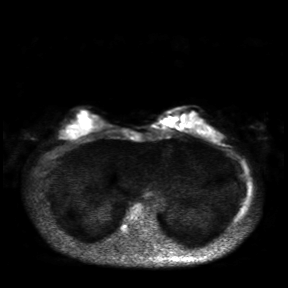
Breast MRI, one axial slice. Position 9 of 30 along the scan axis. Diffusion-weighted series; image 2 of 4 stored at this slice position (different b-values; order by instance number). 3 T. 288 × 288 image matrix, field of view 360 × 360 mm. Female patient.
Outlined on this slice (manually delineated by an expert):
- tumour on diffusion-weighted imaging: bounding box <162,120,173,124> (left, top, right, bottom; pixels)